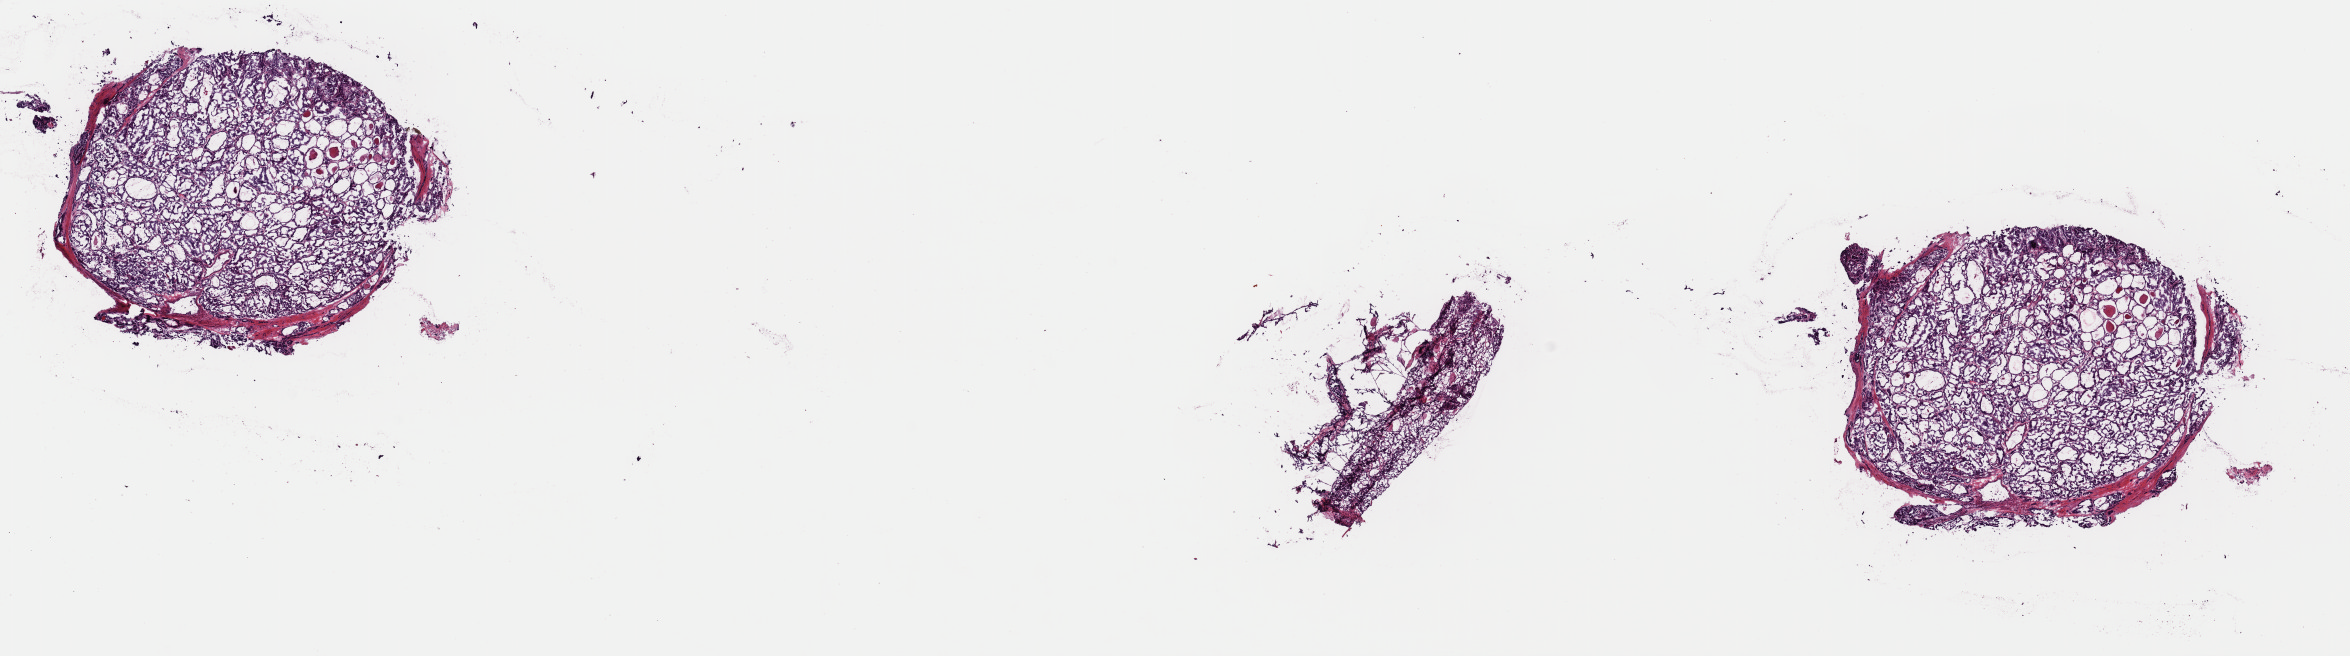
Digitized Hematoxylin and eosin (H&E) stained tissue section (whole slide), low-resolution overview of the scanned area, about 18.6 x 5.2 mm (slide scanned at 40x), frozen section from the top of the tissue portion, thyroid, primary tumour sample. Female patient; age at initial diagnosis 28 years. Composition of this section per pathologist review: tumour cells 90%, tumour nuclei 85%, normal cells 0%, stromal cells 10%, necrosis 0%. Inflammatory infiltration, as recorded: lymphocyte infiltration 2%, monocyte infiltration 1%, neutrophil infiltration 0%.
TNM: T3 N1 M0. Lymph nodes positive (case pathology): 6 of 55 examined. AJCC pathologic stage: I (6th edition). Pathologic diagnosis: Papillary adenocarcinoma, NOS (thyroid gland).